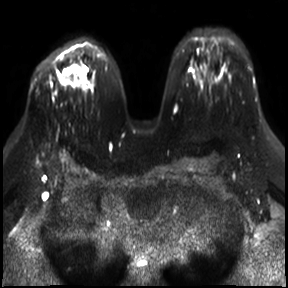
Breast MRI, one axial slice; slice 20 of 30 in the series (ordered by position); diffusion-weighted series; image 2 of 4 stored at this slice position (different b-values; order by instance number); 3 T; 4 mm slice thickness; 288 × 288 image matrix. Female patient.
Annotated regions visible in this slice (manually delineated by an expert):
- tumour on diffusion-weighted imaging: bounding box [x1, y1, x2, y2] px = [64, 70, 66, 72]